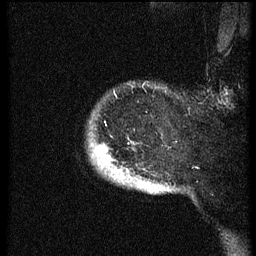
Breast MRI (dynamic contrast-enhanced), one sagittal slice. Slice 55 of 60 in the series (ordered by position). Dynamic contrast-enhanced series, image 2 of 3 at this slice position (ordered by acquisition). 1.5 T. TE 4.2 ms, TR 8.4 ms. 2.5 mm slice thickness. 256 × 256 image matrix, field of view 200 × 200 mm. Female patient, age 38 years. From the clinical record (not read from this slice): setting: breast cancer imaged before/during neoadjuvant chemotherapy; receptor status: HER2-positive.
Annotated regions visible in this slice (semi-automatic segmentation, software-assisted and operator-edited):
- analysis volume of interest (the breast-tissue region the enhancement analysis was run in; not a lesion): bounding box [x1, y1, x2, y2] px = [90, 91, 173, 194]
- tumour enhancement mask (voxels above the 70 % enhancement threshold inside the analysis volume of interest): [98, 147, 124, 179]